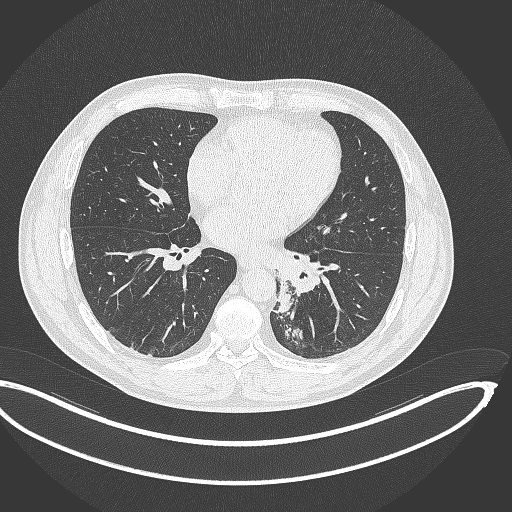
Chest CT, one axial slice; reconstruction kernel B70f; lung window (W 1500 / L -600 HU); 1 mm slice thickness; 512 × 512 image matrix, field of view 442 × 442 mm. Patient: male, 50 years. From the clinical record (not read from this slice): clinical TNM (as recorded): T2a N3 M0.
Annotated regions visible in this slice (rectangle marked by the reading radiologist):
- lung tumour (recorded histology: squamous cell carcinoma): bounding box [x1, y1, x2, y2] px = [273, 281, 294, 313]